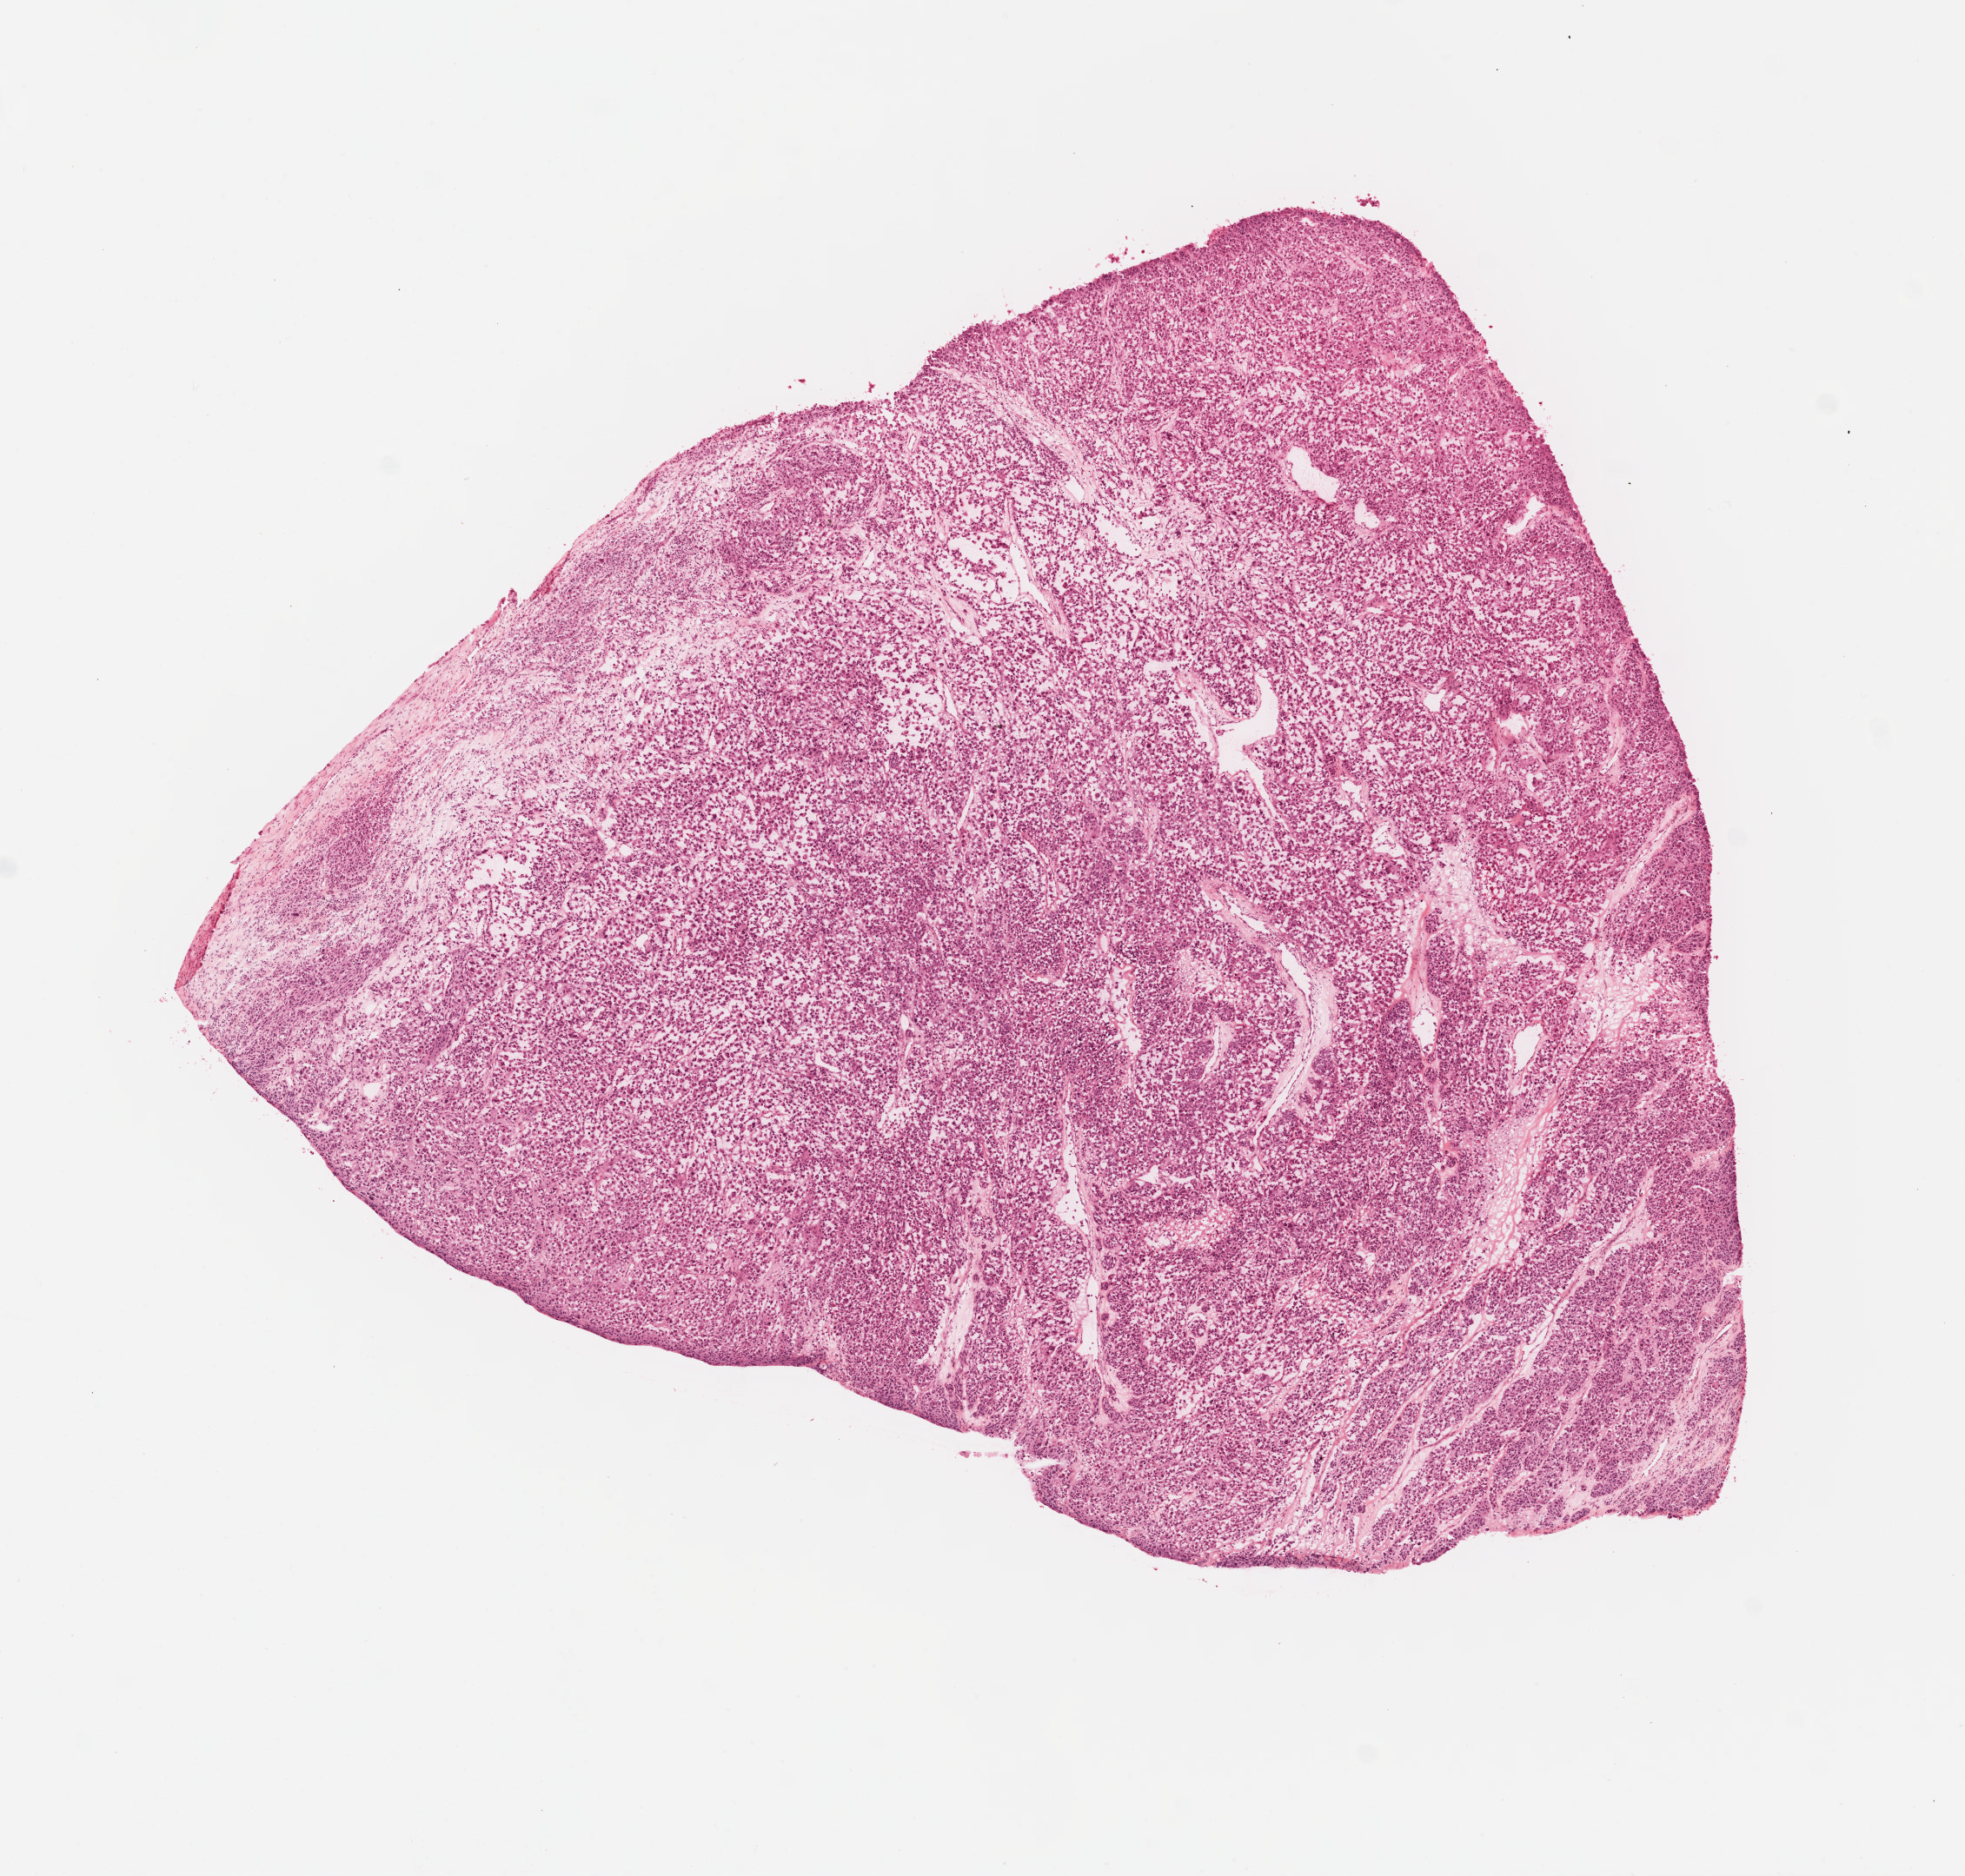
H&E whole-slide image, a low-resolution overview of the entire scanned area, about 8.9 x 8.5 mm, formalin-fixed paraffin-embedded (FFPE) diagnostic section, sample: primary tumour, skin. Male patient; age at initial diagnosis 43 years.
Diagnosis: Malignant melanoma, NOS.